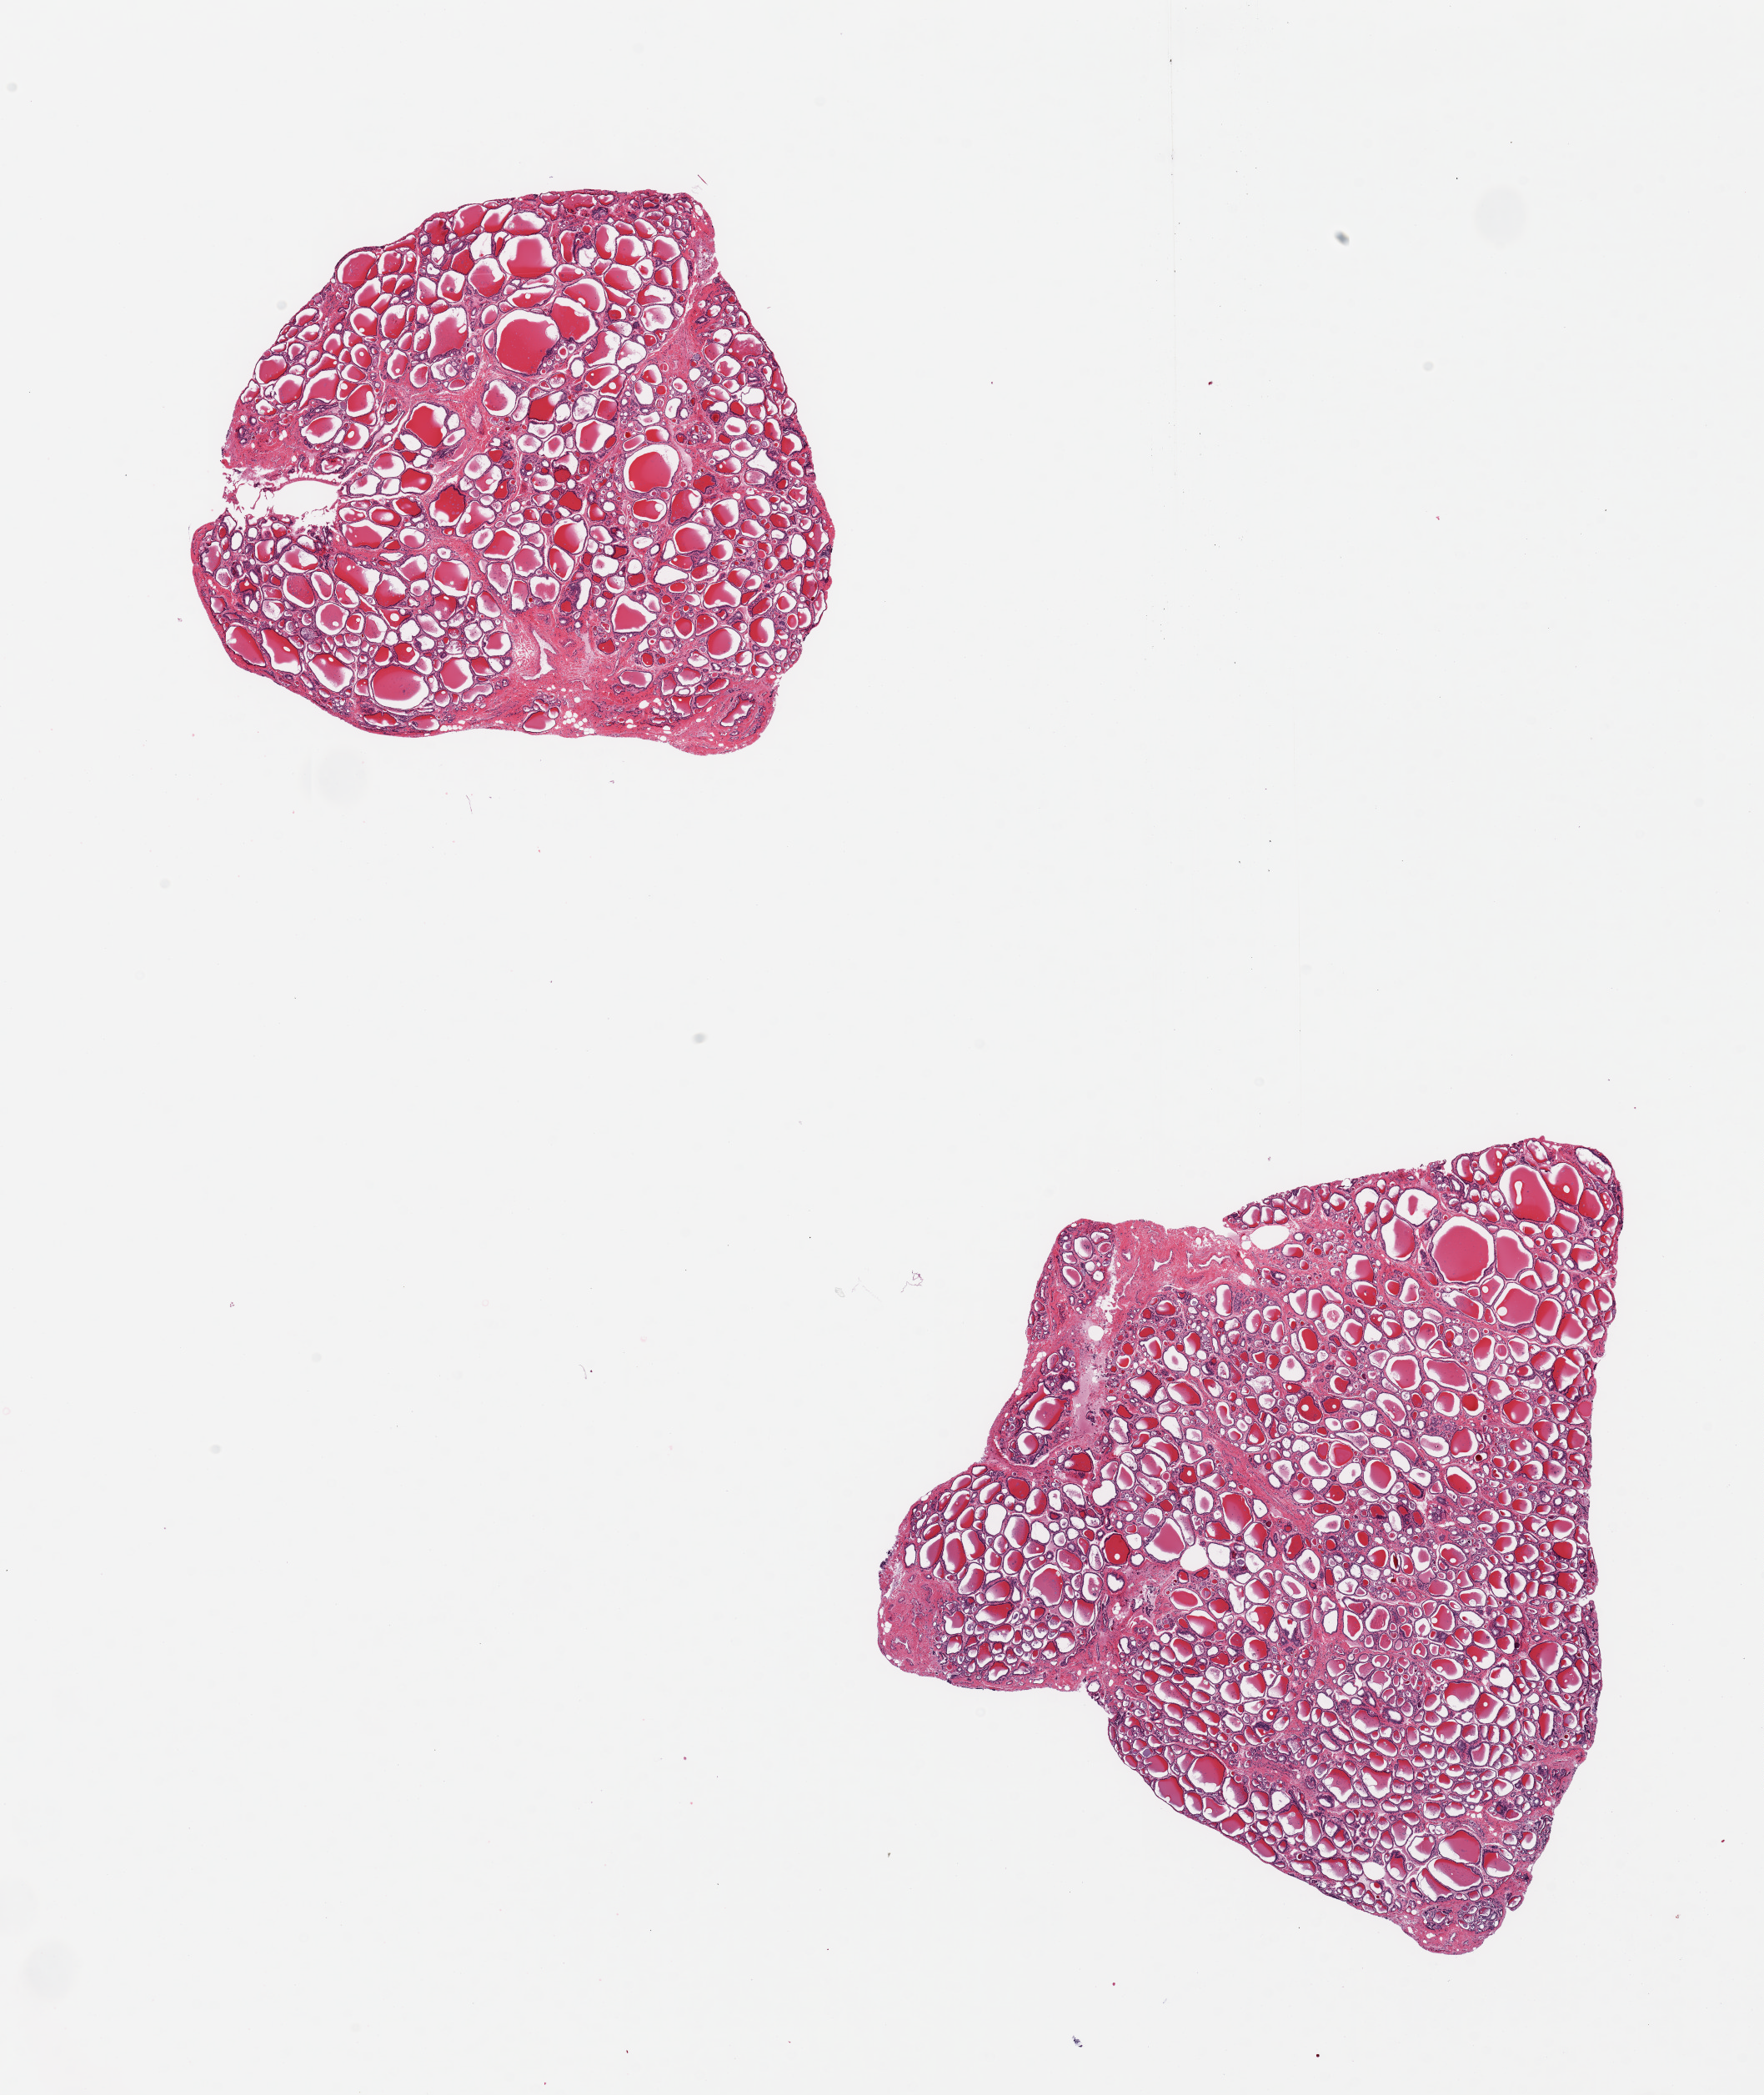
Digitized haematoxylin and eosin-stained section, whole scanned area (about 16.7 x 19.9 mm) shown as a low-resolution overview; PAXgene-fixed, paraffin-embedded tissue; target tissue: thyroid; donor tissue sample. Male donor.
Review note (as recorded): 2 pieces, no abnormalities.